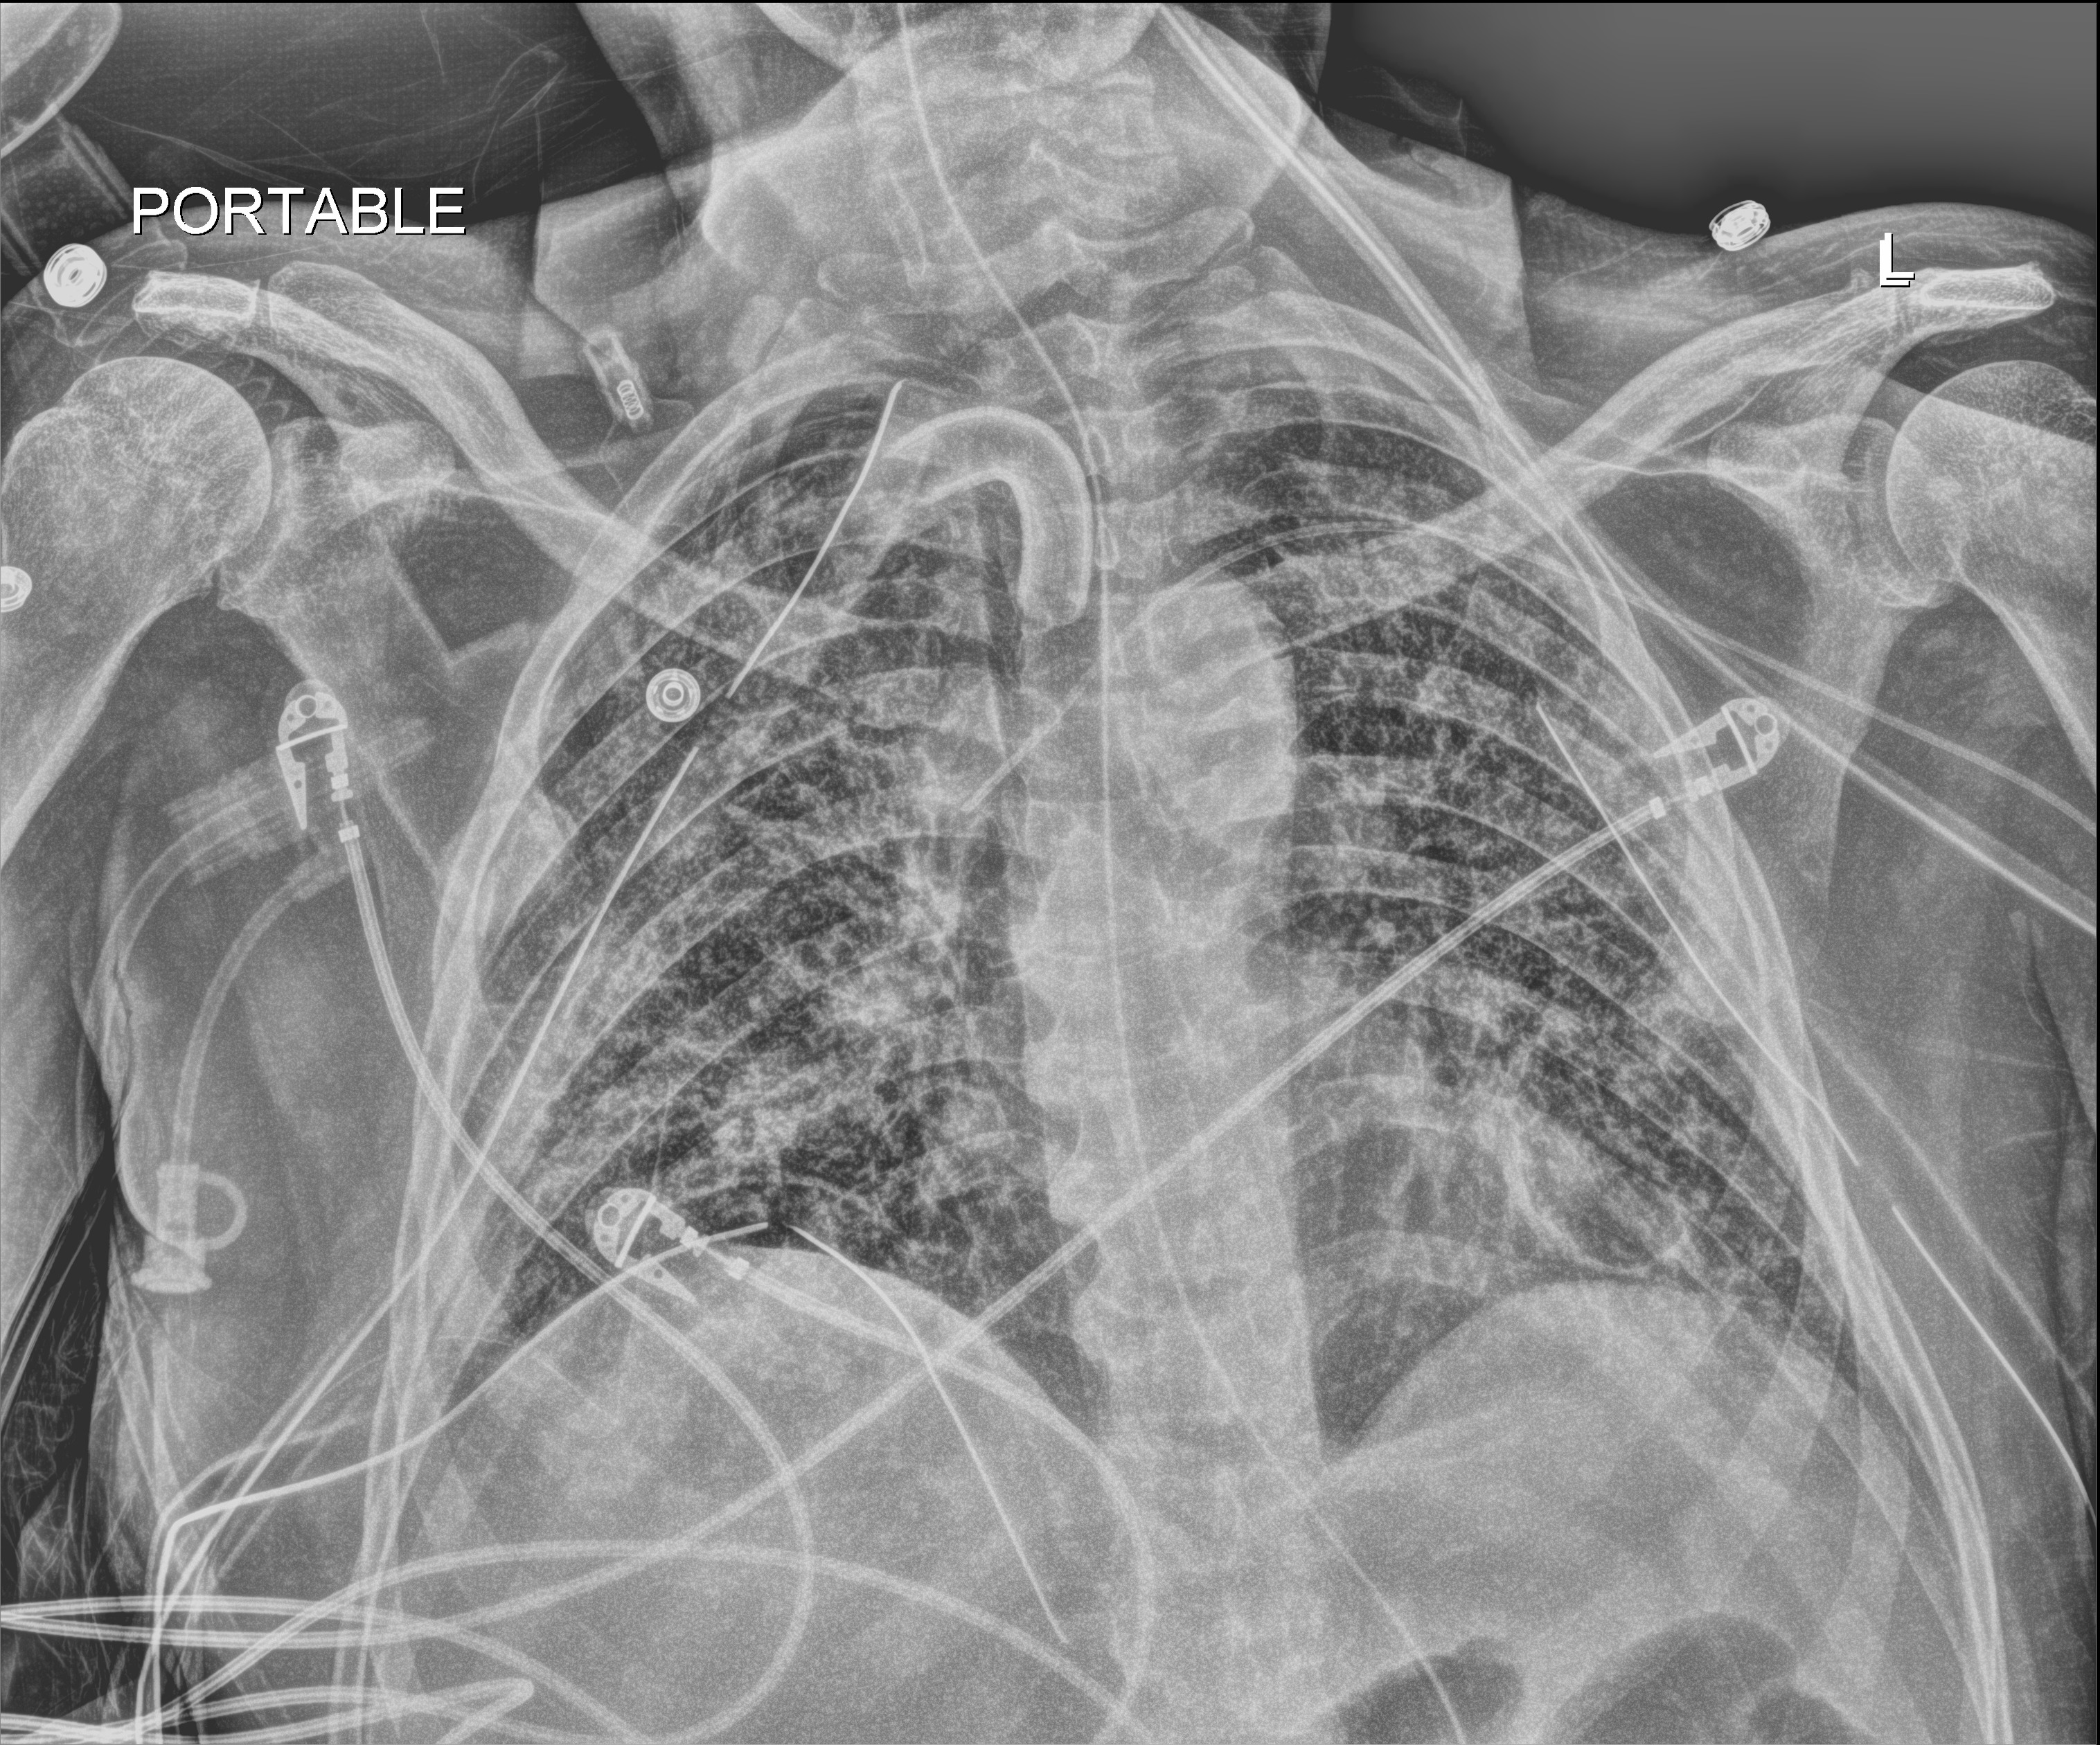
Portable chest radiograph. Male patient hospitalised with COVID-19, age 18–59 years.
From the hospital-stay record, not from the radiograph (when in the stay this image was taken is not recorded): smoking status (admission record): never.